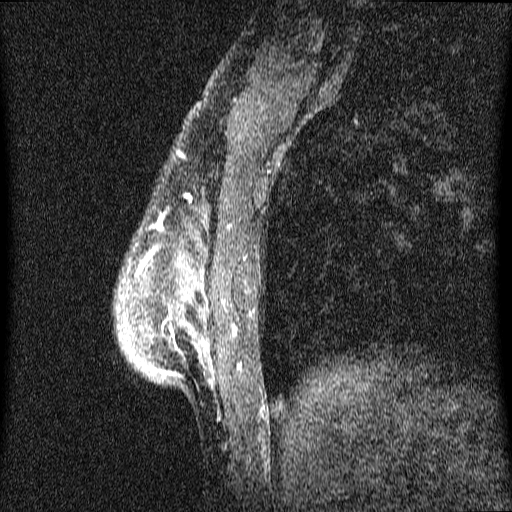
Breast MRI (dynamic contrast-enhanced), one sagittal slice; slice 14 of 64 in the series (ordered by position); dynamic contrast-enhanced series, image 2 of 4 at this slice position (ordered by acquisition); 1.5 T; TE 4.2 ms, TR 9.1 ms; 2 mm slice thickness; 512 × 512 image matrix, field of view 180 × 180 mm. Female patient, age 33 years.
Outlined on this slice (semi-automatically segmented with operator editing):
- analysis volume of interest (the breast-tissue region the enhancement analysis was run in; not a lesion): bounding box [x1, y1, x2, y2] px = [116, 157, 259, 418]
- tumour enhancement mask (voxels above the 70 % enhancement threshold inside the analysis volume of interest): [140, 262, 174, 373]